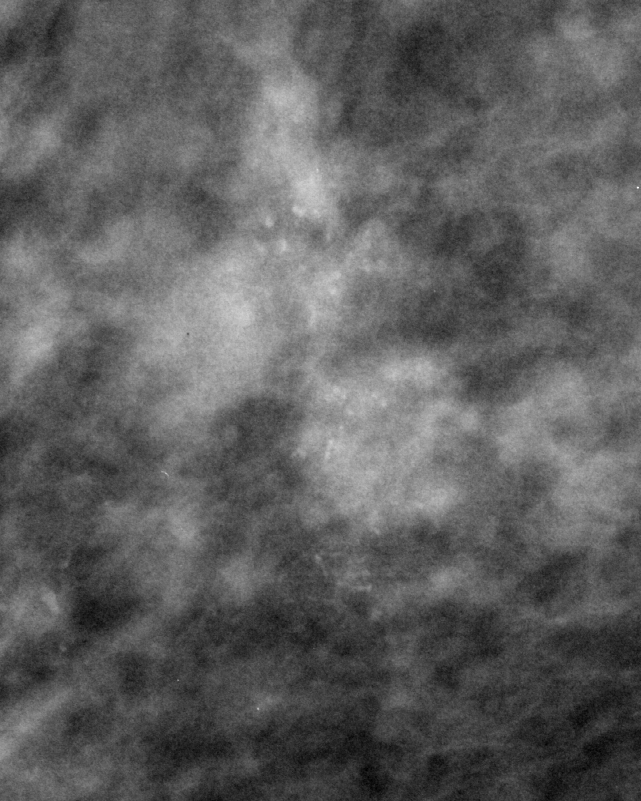
Region of interest cut from a scanned film mammogram (one marked finding), right breast, MLO view, BI-RADS breast density category 2 (scale 1–4).
Calcifications, morphology pleomorphic, distribution clustered; BI-RADS assessment category 5; subtlety rating 5 on a 1 (subtle) to 5 (obvious) scale; pathology (as recorded): malignant.